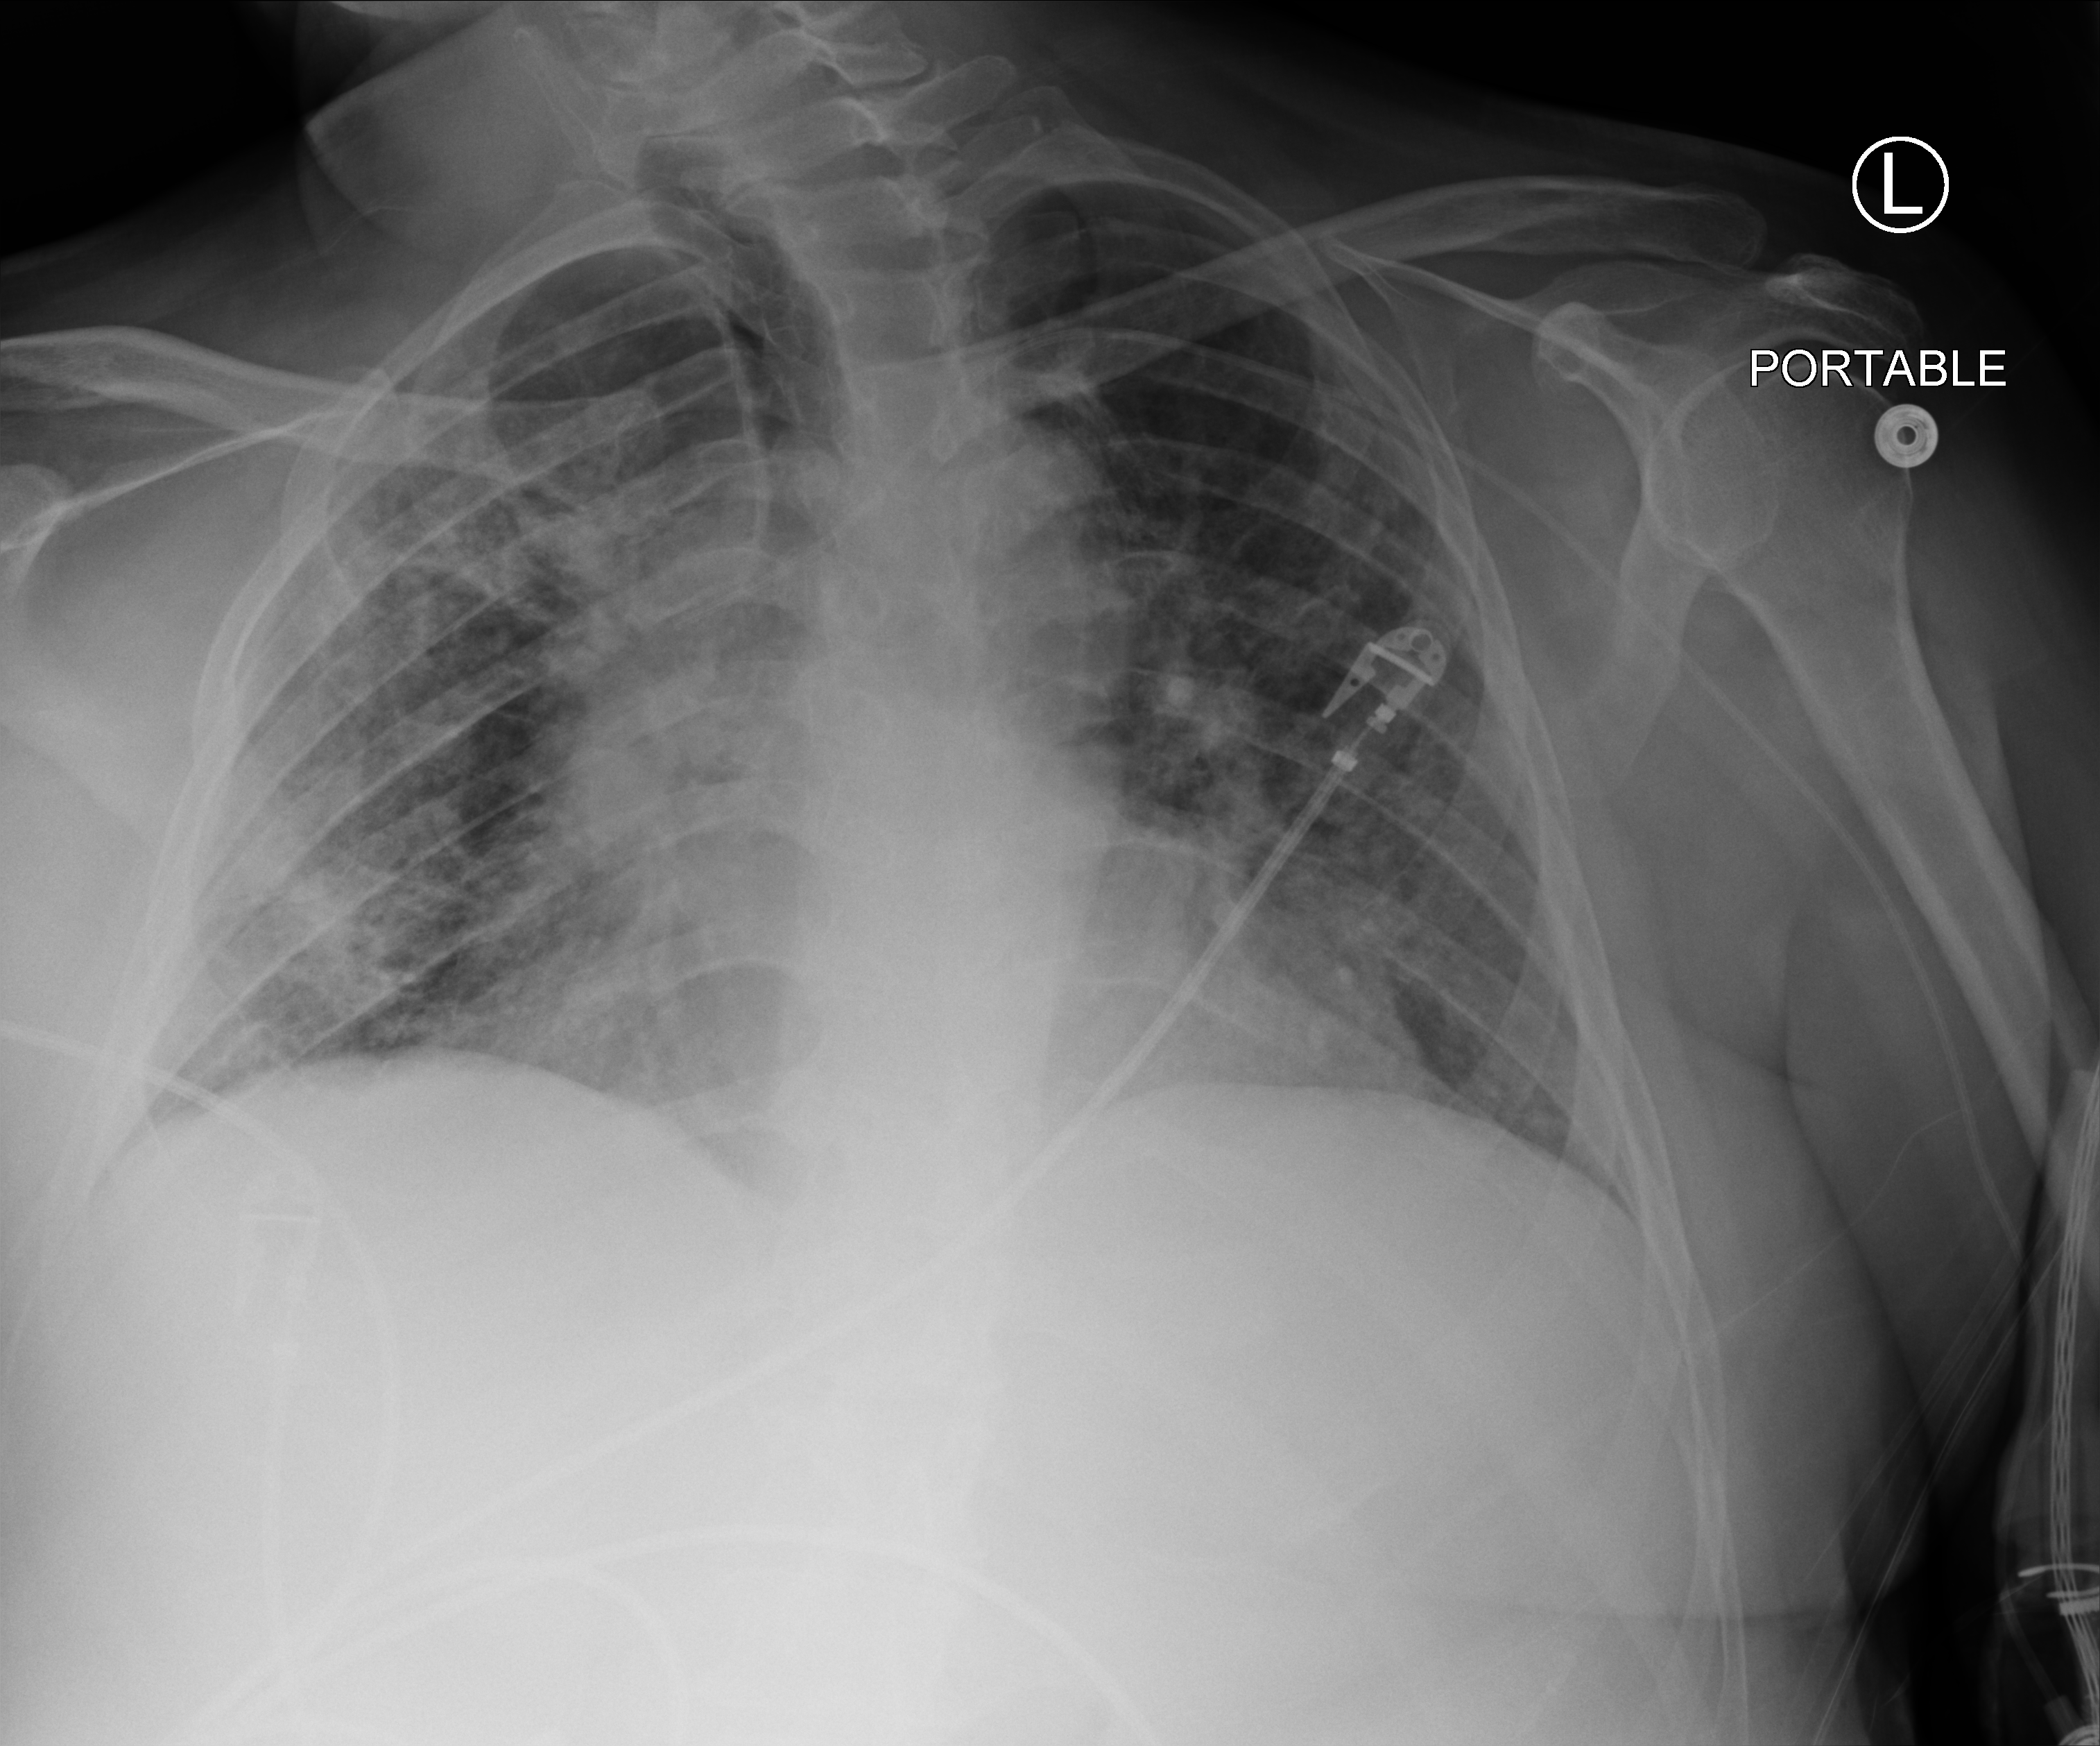
Portable chest radiograph. Patient hospitalised with COVID-19; male, aged 18–59 years.
From the hospital-stay record, not from the radiograph (when in the stay this image was taken is not recorded): mechanically ventilated during this hospital stay: yes; admitted to intensive care during this hospital stay: yes; hypertension (admission record): yes.